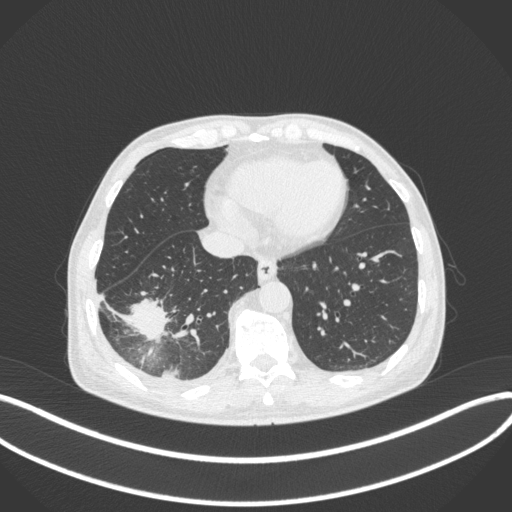
Chest CT, one axial slice; position 109 of 385 along the scan axis; reconstruction kernel B31f; 120 kVp; lung window (W 1500 / L -600 HU); 1 mm slice thickness; 512 × 512 image matrix, field of view 400 × 400 mm. Patient: male, 64 years. From the clinical record (not read from this slice): clinical TNM (as recorded): T3 N0 M0.
Outlined on this slice (rectangle marked by the reading radiologist):
- lung tumour (recorded histology: adenocarcinoma): bounding box [x1, y1, x2, y2] px = [124, 290, 171, 347]